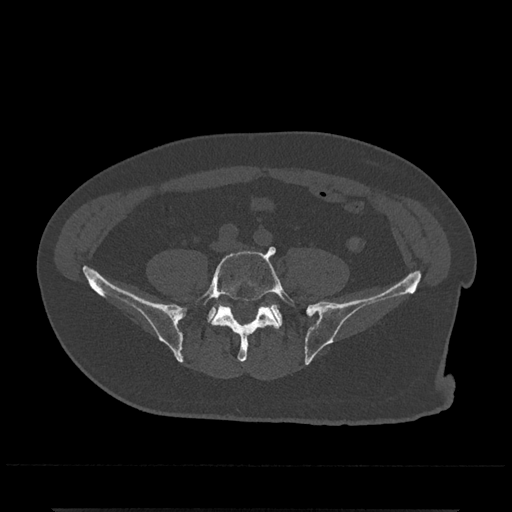
CT including the spine, one axial slice. Slice 80 of 797 in the series (ordered by position). Bone window (W 1800 / L 400 HU). 0.5 mm slice thickness. 512 × 512 image matrix. Patient: male, 67 years. From the clinical record (not read from this slice): primary cancer: prostate.
Outlined on this slice (semi-automatic segmentation, software-assisted and operator-edited):
- L5 vertebra: bounding box [x1, y1, x2, y2] px = [195, 247, 295, 362]